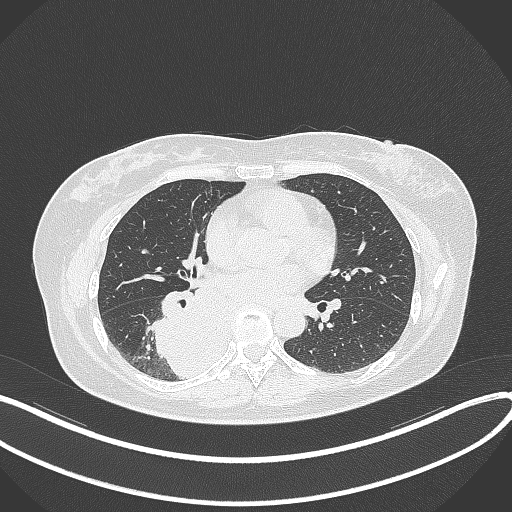
Chest CT, one axial slice. Position 171 of 331 along the scan axis. Reconstruction kernel B70f. Lung window (W 1500 / L -600 HU). 1 mm slice thickness. 512 × 512 image matrix, field of view 400 × 400 mm. Female patient, age 54 years. Case-level facts recorded for this patient, not image findings: clinical TNM (as recorded): T4 N0 M0.
Outlined on this slice (rectangle marked by the reading radiologist):
- lung tumour (recorded histology: adenocarcinoma): bounding box <147,289,237,384> (left, top, right, bottom; pixels)